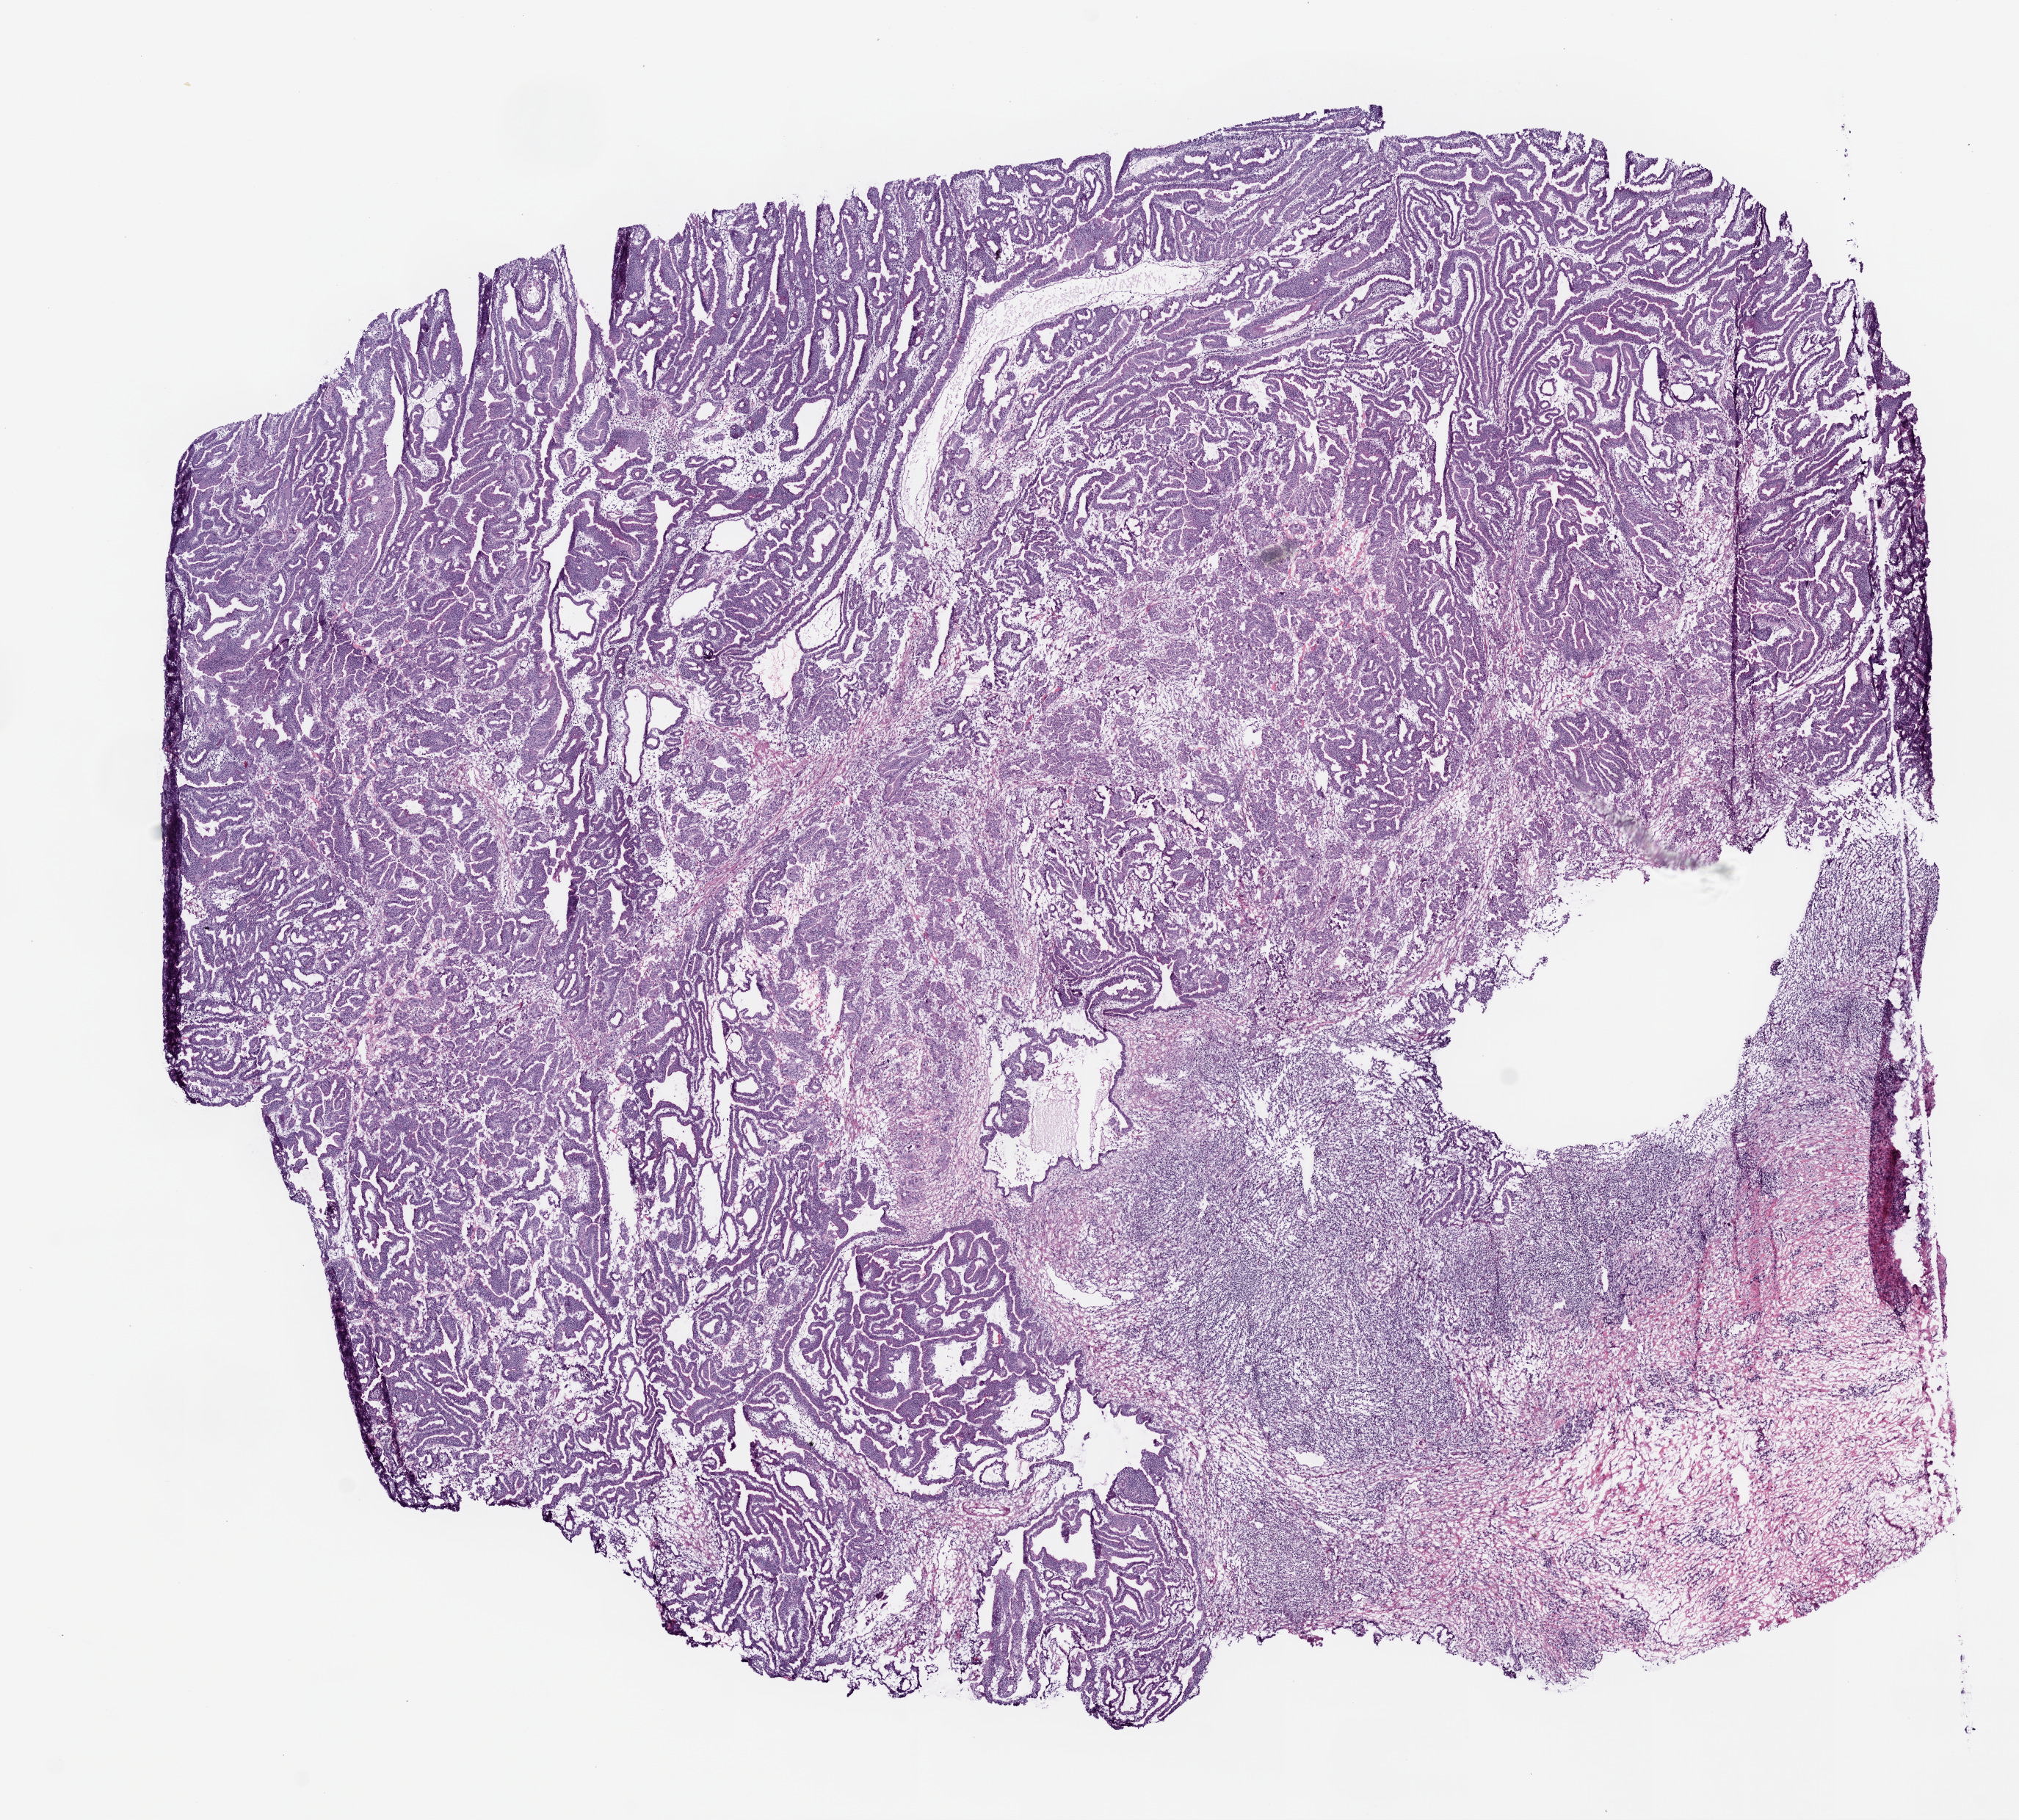
H&E whole-slide image — shown as a low-resolution overview of the whole scanned area (about 11.0 x 9.9 mm); frozen section from the bottom of the tissue portion; stomach, primary tumour sample. Male patient; age at initial diagnosis 84 years. Histologic grade: G2 (moderately differentiated). Composition of this section per pathologist review: tumour cells 80%, tumour nuclei 70%, normal cells 0%, stromal cells 20%, necrosis 0%. Inflammatory infiltration, as recorded: lymphocyte infiltration 20%, monocyte infiltration 0%, neutrophil infiltration 0%.
AJCC pathologic stage: IB (6th edition). Histologic diagnosis: Adenocarcinoma, NOS (cardia, NOS). Lymph nodes positive (case pathology): 0 of 18 examined.